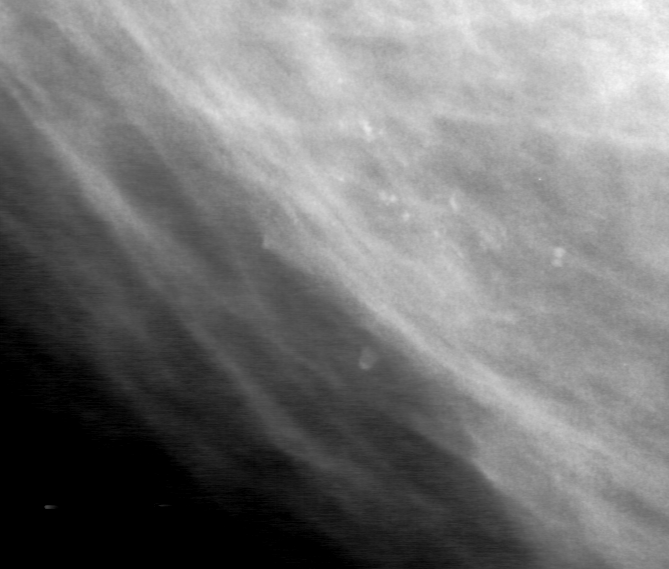
Crop from a digitized film mammogram around one marked abnormality, left breast, MLO view, BI-RADS breast density category 3 (scale 1–4).
Calcifications, morphology punctate / fine linear branching, distribution clustered; BI-RADS assessment category 0 (incomplete: needs additional imaging); subtlety rating 4 on a 1 (subtle) to 5 (obvious) scale; pathology (as recorded): malignant.